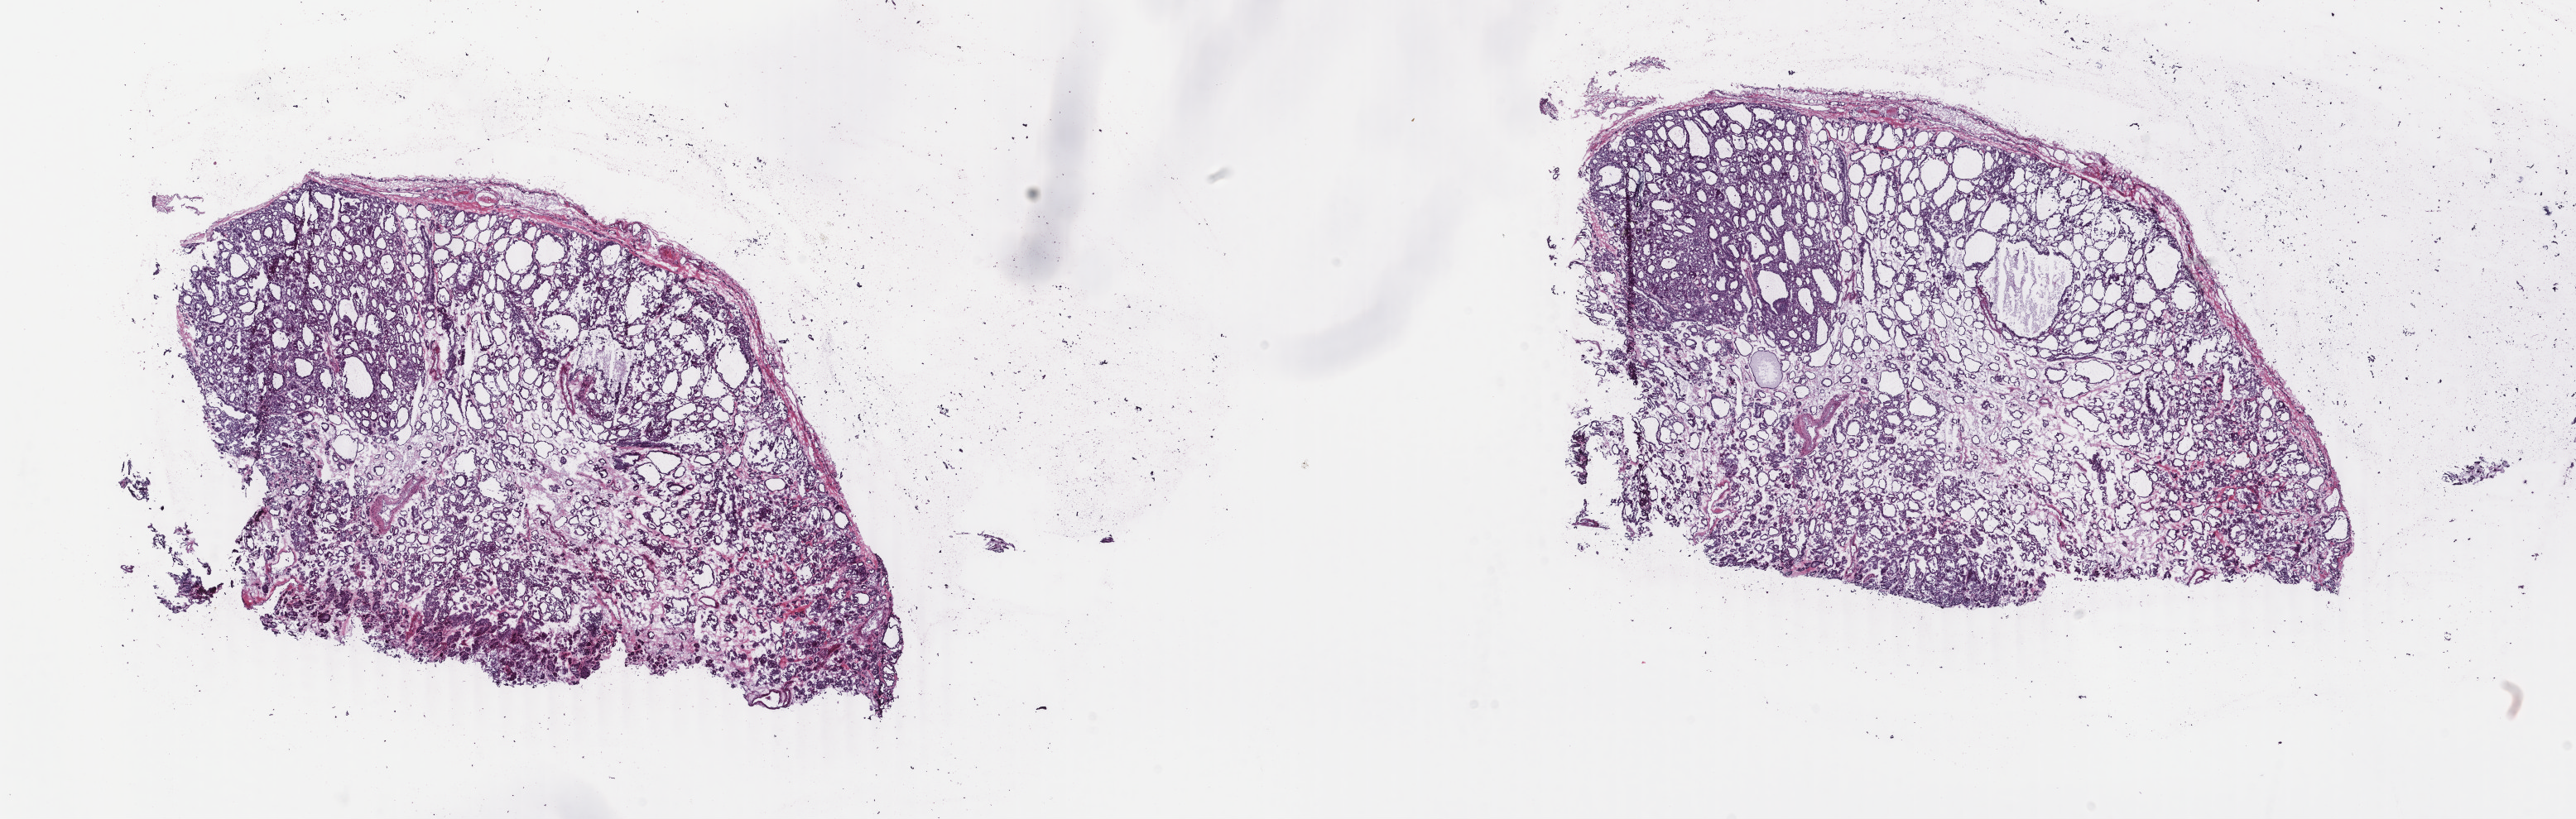
Digitized H&E tissue section (whole slide), shown as a low-resolution overview of the whole scanned area (about 24.7 x 7.9 mm). Frozen section from the top of the tissue portion. Primary tumour sample from the thyroid. Male, age 55 years at initial diagnosis. Pathologist review of this section (percent, as recorded): tumour cells 85%, tumour nuclei 85%, normal cells 0%, stromal cells 15%, necrosis 0%. Infiltration values recorded for this section: lymphocyte infiltration 1%, monocyte infiltration 0%, neutrophil infiltration 0%.
Laterality: bilateral. AJCC pathologic stage: II (7th edition). Lymph nodes positive (case pathology): 0 of 1 examined. Diagnosis: Papillary adenocarcinoma, NOS (thyroid gland).